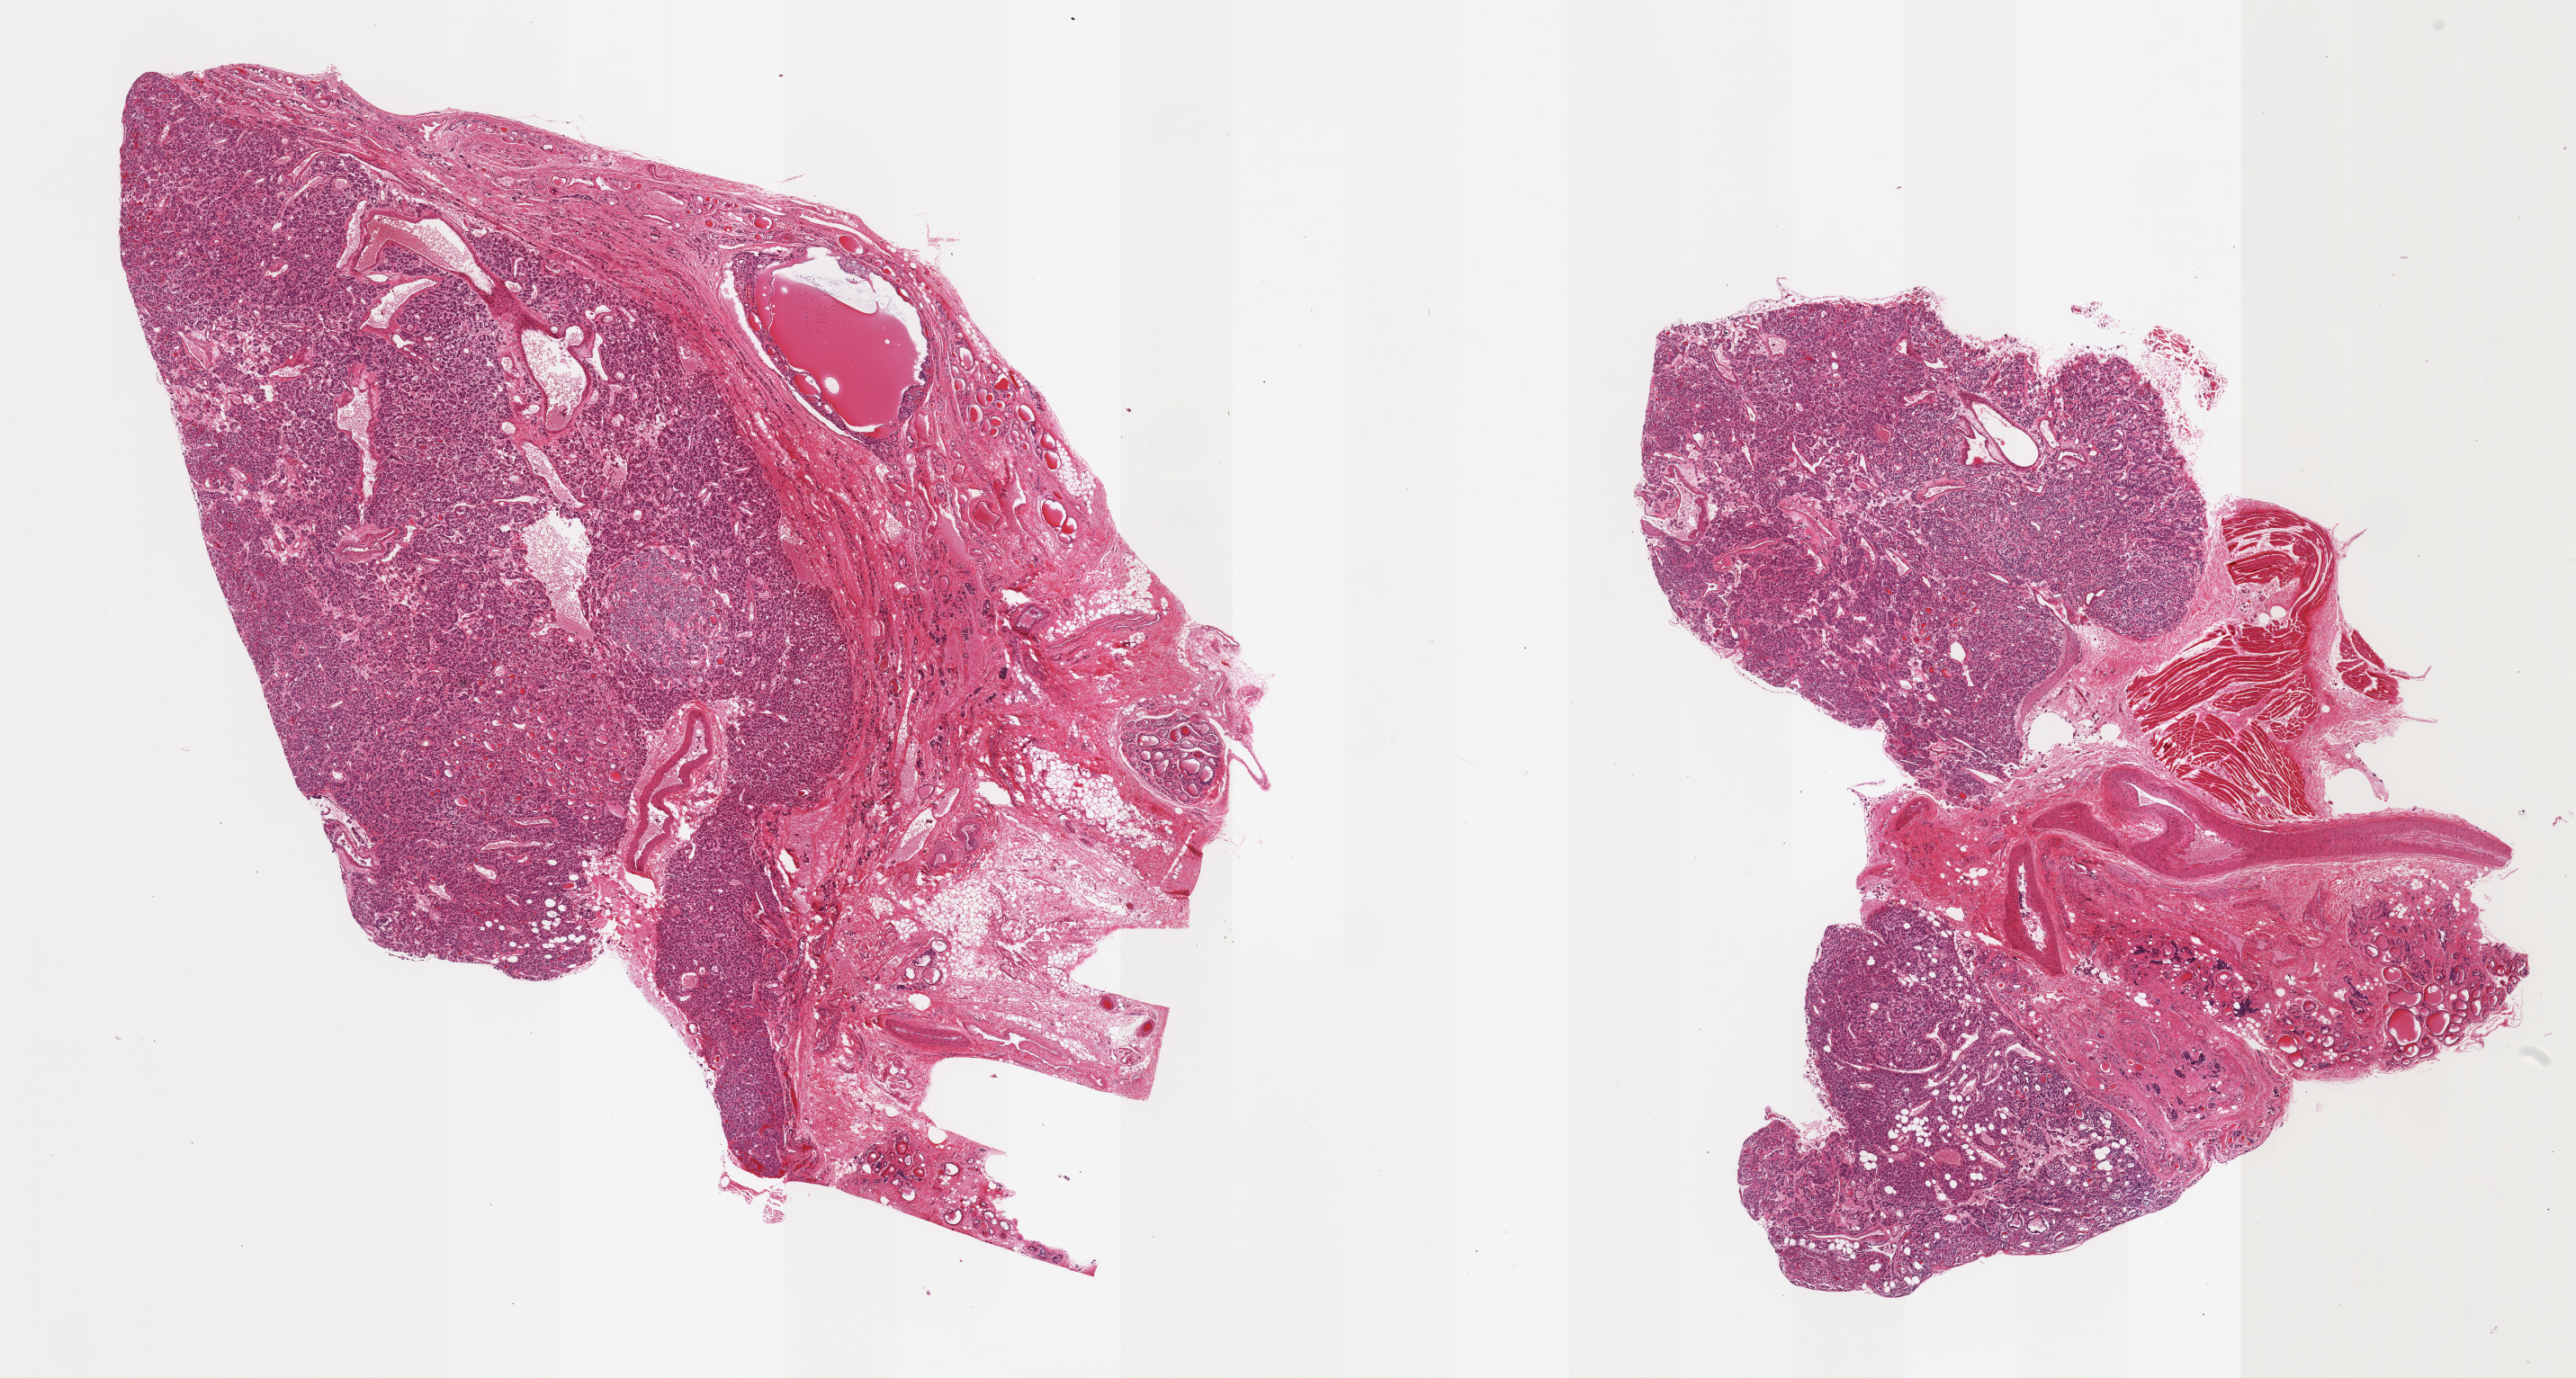
Whole-slide image, H&E stain — low-resolution overview of the scanned area, about 22.6 x 12.1 mm (slide scanned at 20x); PAXgene-fixed paraffin-embedded (PFPE) section; target tissue: thyroid; donor tissue sample.
Review note (as recorded): 2 pieces; possible neoplasm; needs expert consultation.